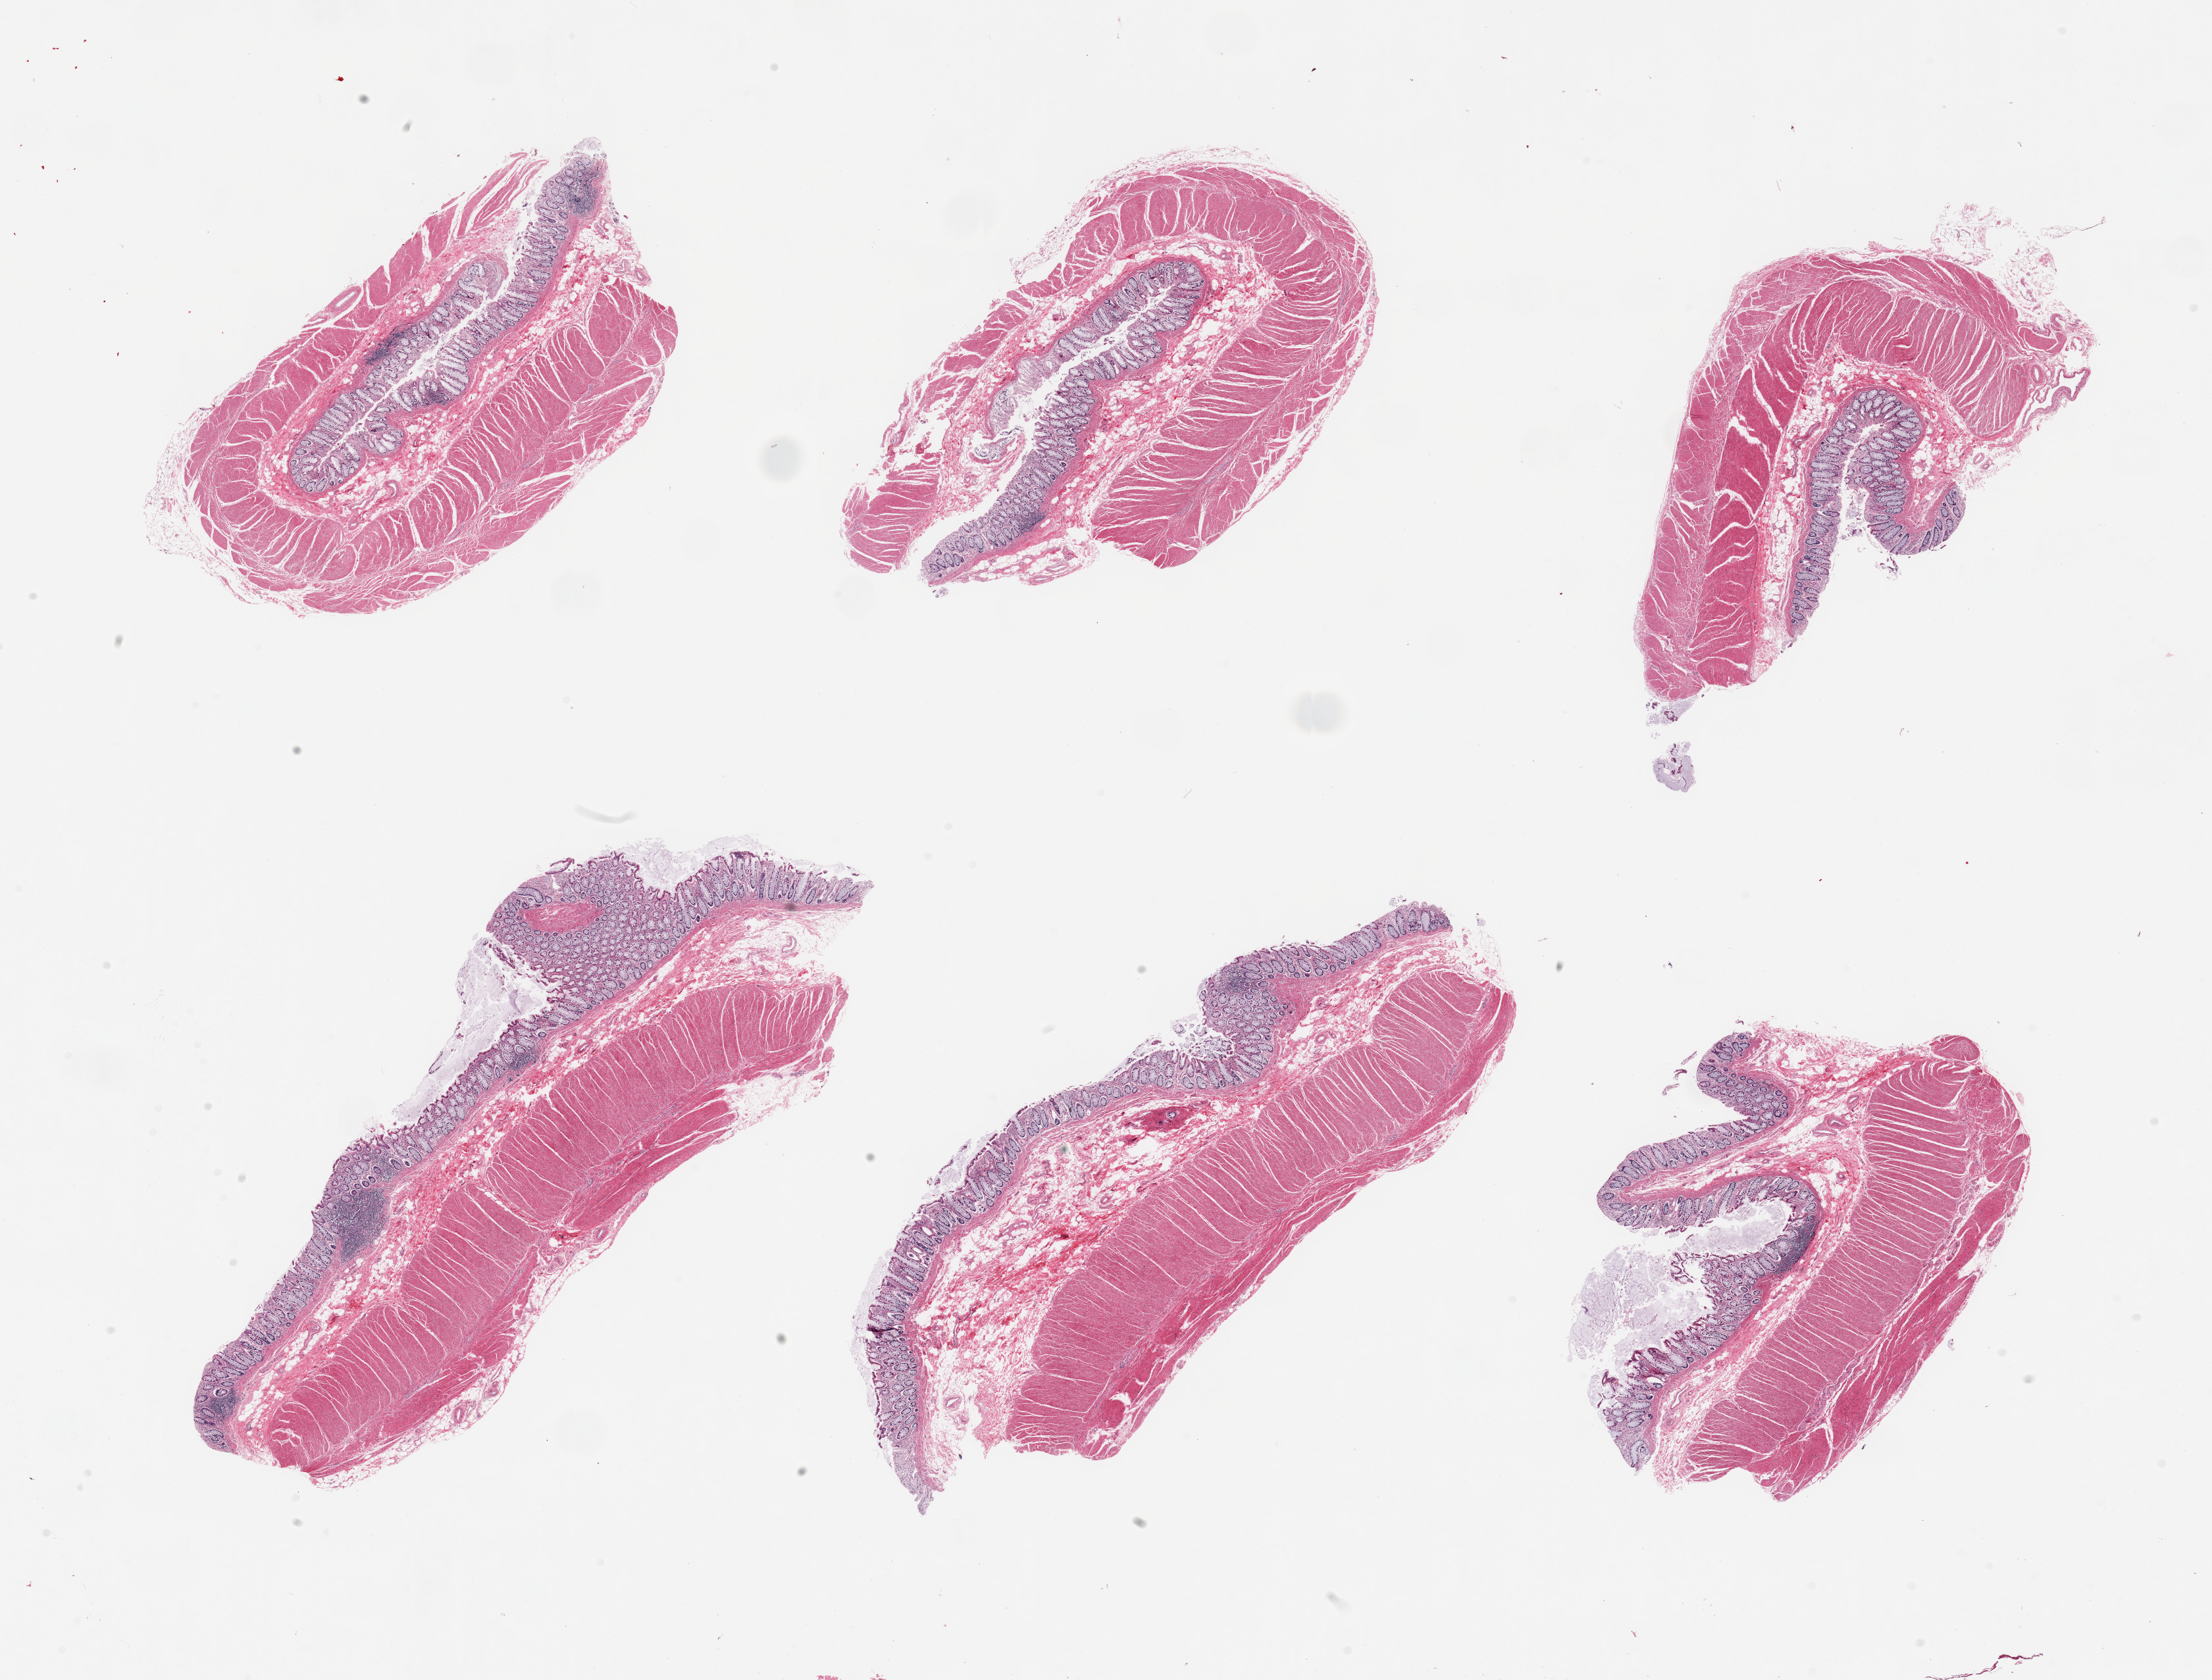
Digitized hematoxylin and eosin (H&E)-stained section, brightfield, low-resolution overview of the scanned area, about 26.6 x 20.2 mm (from a 20x scan). Female donor.
Specimen: PAXgene-fixed, paraffin-embedded tissue; sampled site (target tissue): sigmoid colon; tissue donor sample.